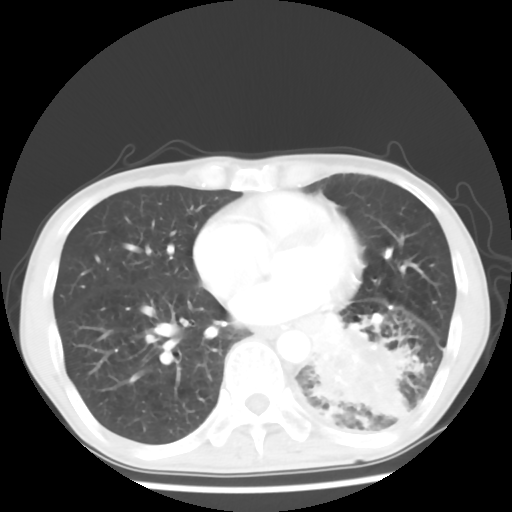
Chest CT, one axial slice; position 25 of 64 along the scan axis; reconstruction kernel STANDARD; lung window (W 1500 / L -600 HU); 512 × 512 image matrix. Patient: male, 68 years. Case-level facts recorded for this patient, not image findings: clinical TNM (as recorded): T4 N0 M0.
Structures marked on this image (rectangle marked by the reading radiologist):
- lung tumour (recorded histology: squamous cell carcinoma): box from (x=310, y=315) to (x=429, y=433) px